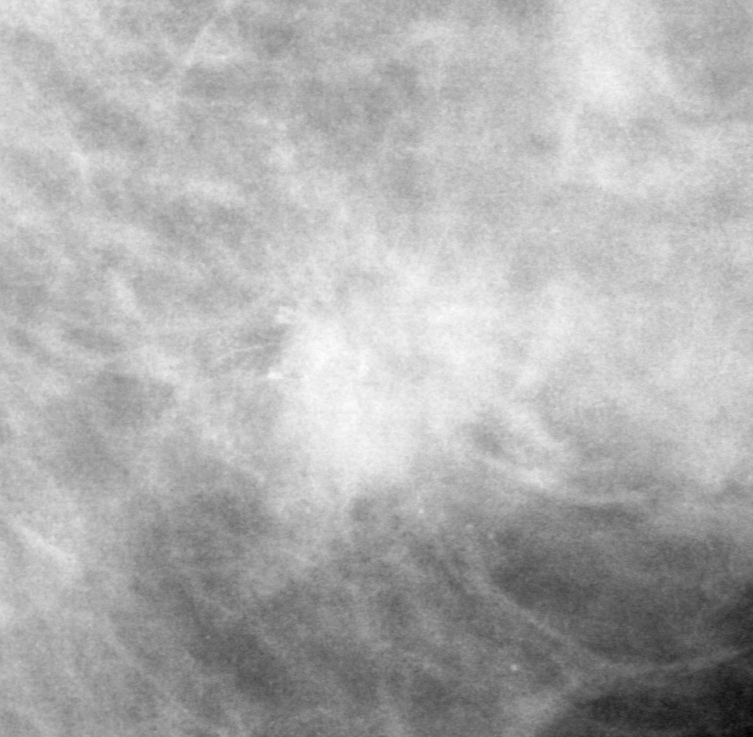
Region of interest cut from a scanned film mammogram (one marked finding); right breast; MLO view.
Finding: calcifications, morphology pleomorphic, distribution clustered; BI-RADS assessment category 5; pathology (as recorded): malignant.